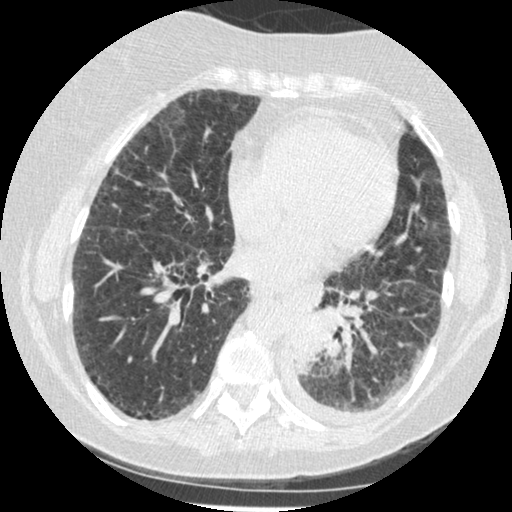
Low-dose screening chest CT, one axial slice. Position 87 of 341 along the scan axis. Reconstruction kernel STANDARD. Lung window (W 1500 / L -600 HU). 512 × 512 image matrix.
Outlined on this slice (manually delineated by an expert):
- lesion 1 (tumor, lower lobe of left lung): bounding box <291,317,324,373> (left, top, right, bottom; pixels)